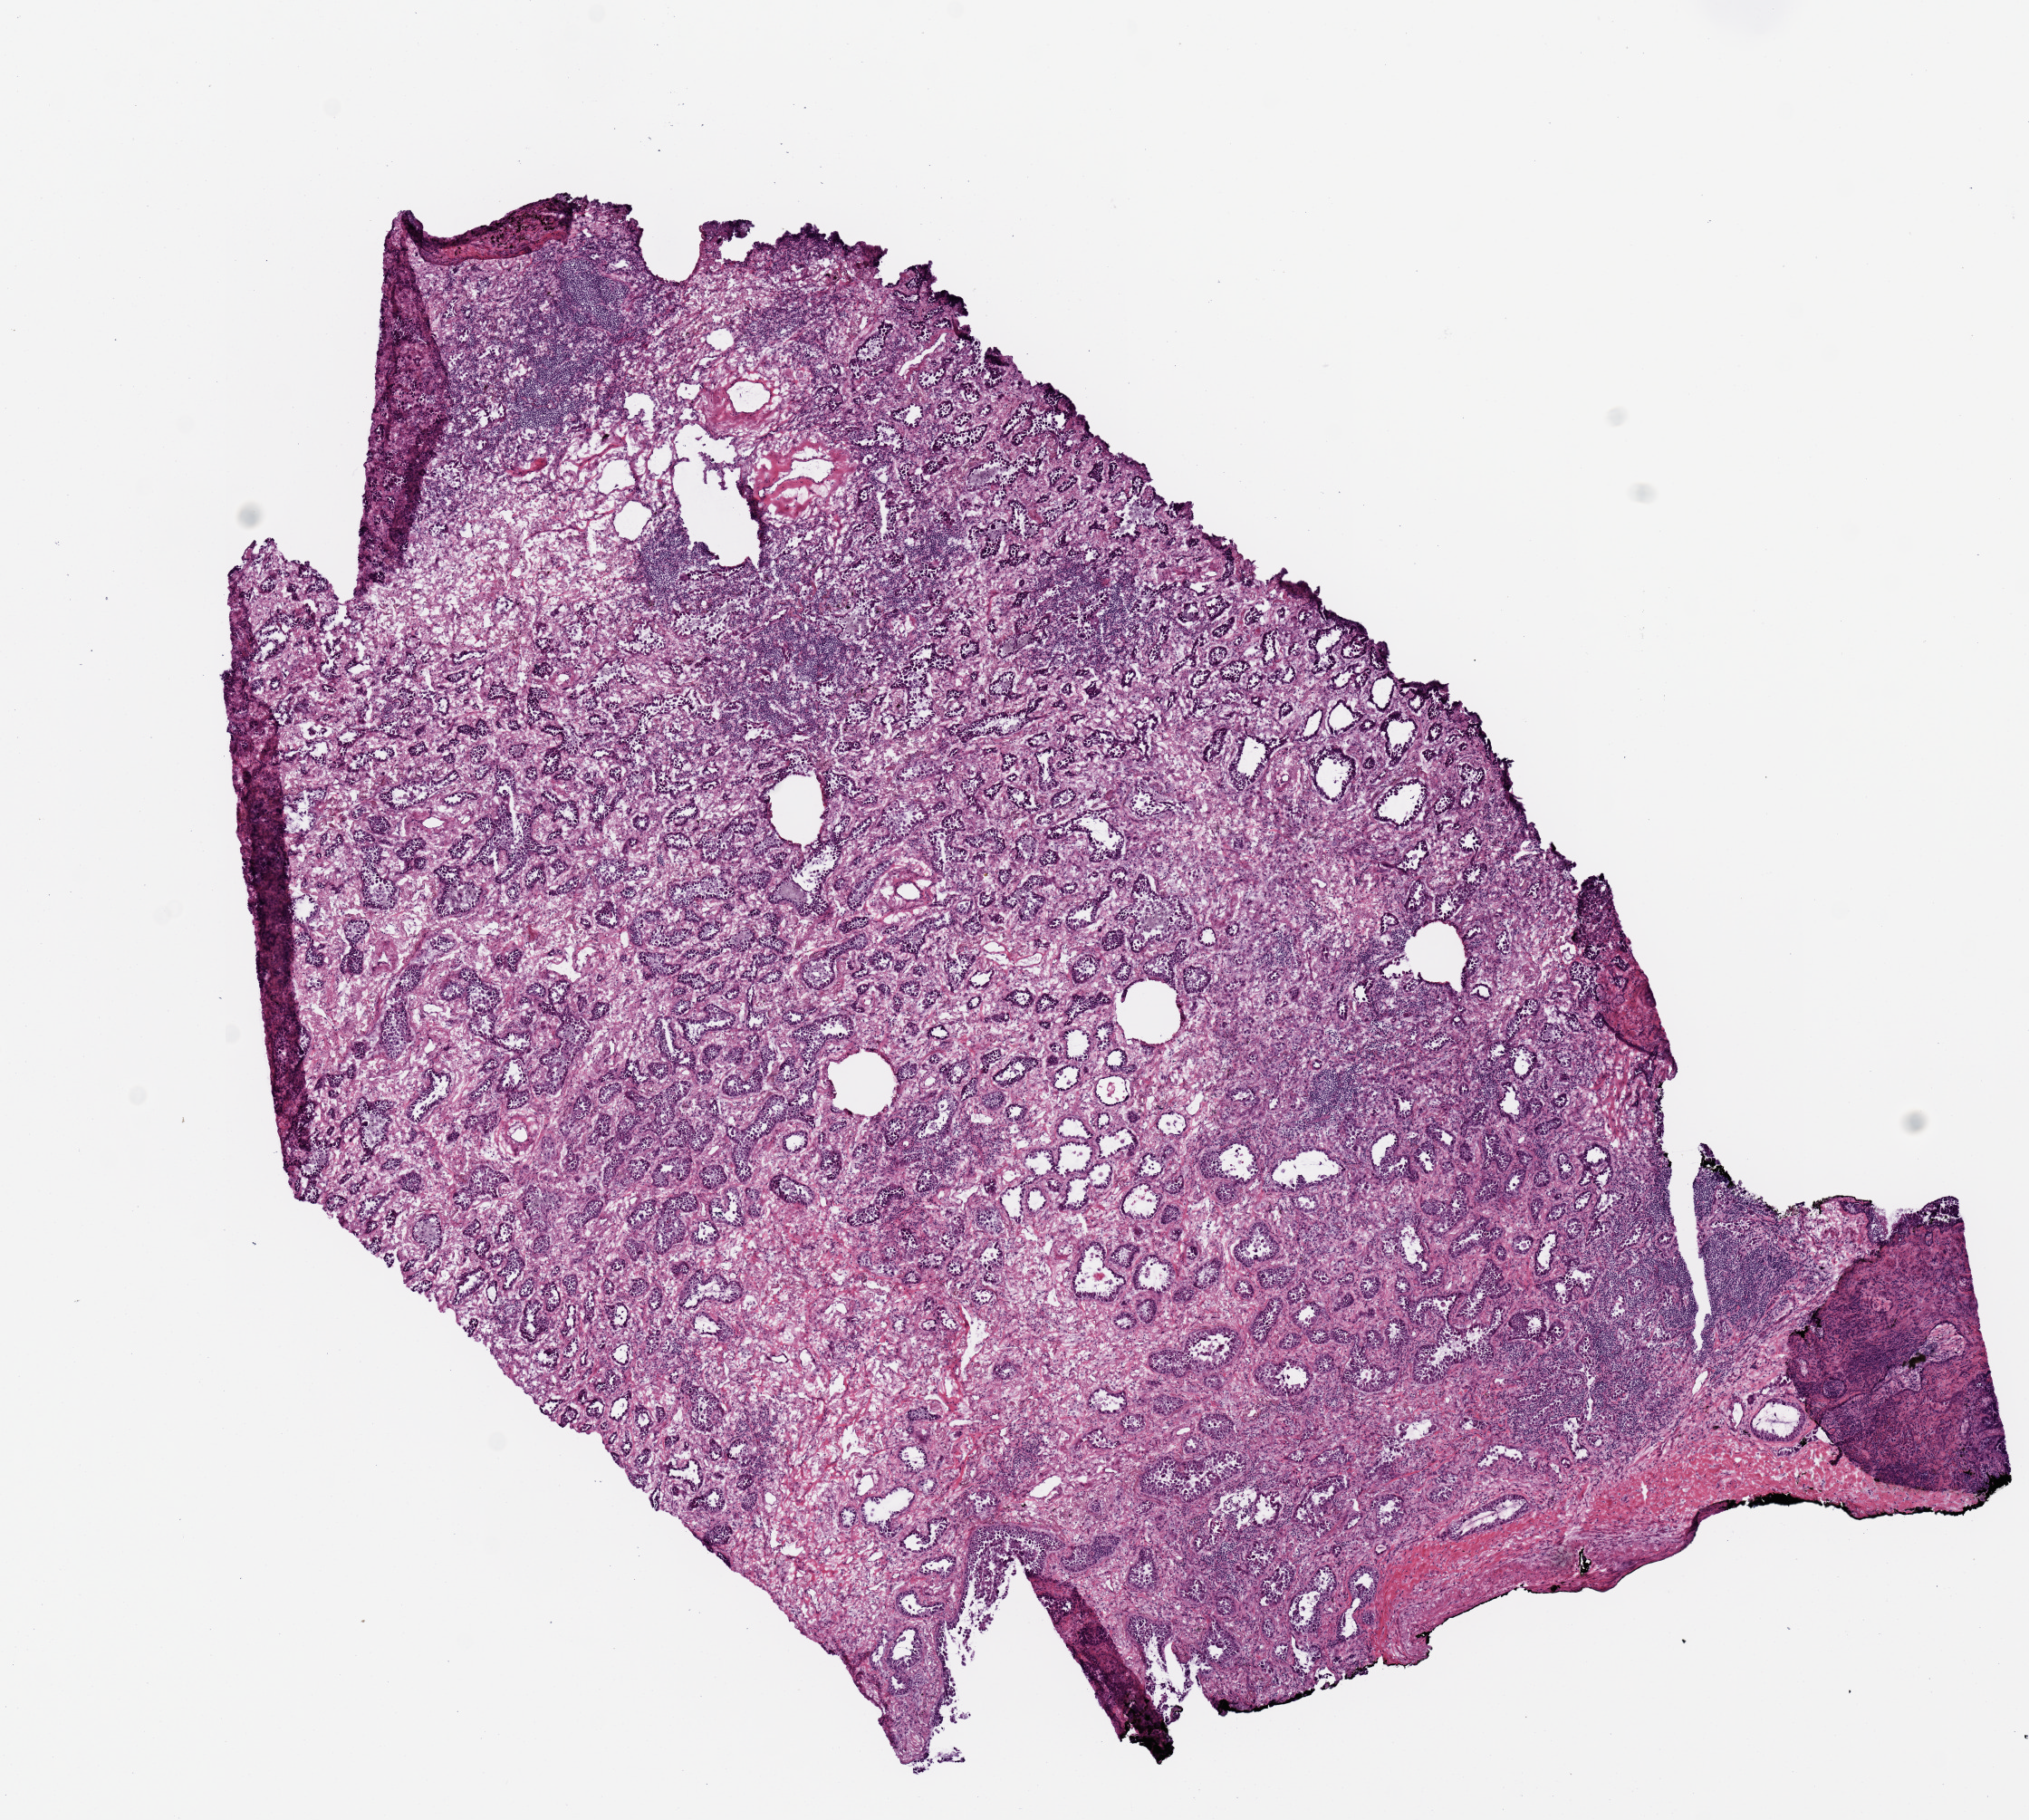
Whole-slide histology image, H&E — shown as a low-resolution overview of the whole scanned area (about 8.9 x 7.9 mm). Frozen section from the top of the tissue portion. Primary tumour sample from the lung. Female patient; age at initial diagnosis 58 years. Composition of this section per pathologist review: tumour cells 100%, tumour nuclei 80%, normal cells 0%, stromal cells 0%, necrosis 0%. Inflammatory infiltration, as recorded: lymphocyte infiltration 5%, monocyte infiltration 0%, neutrophil infiltration 0%.
AJCC pathologic stage: IB (7th edition). Laterality: right. Pathologic diagnosis: Adenocarcinoma, NOS (upper lobe, lung).